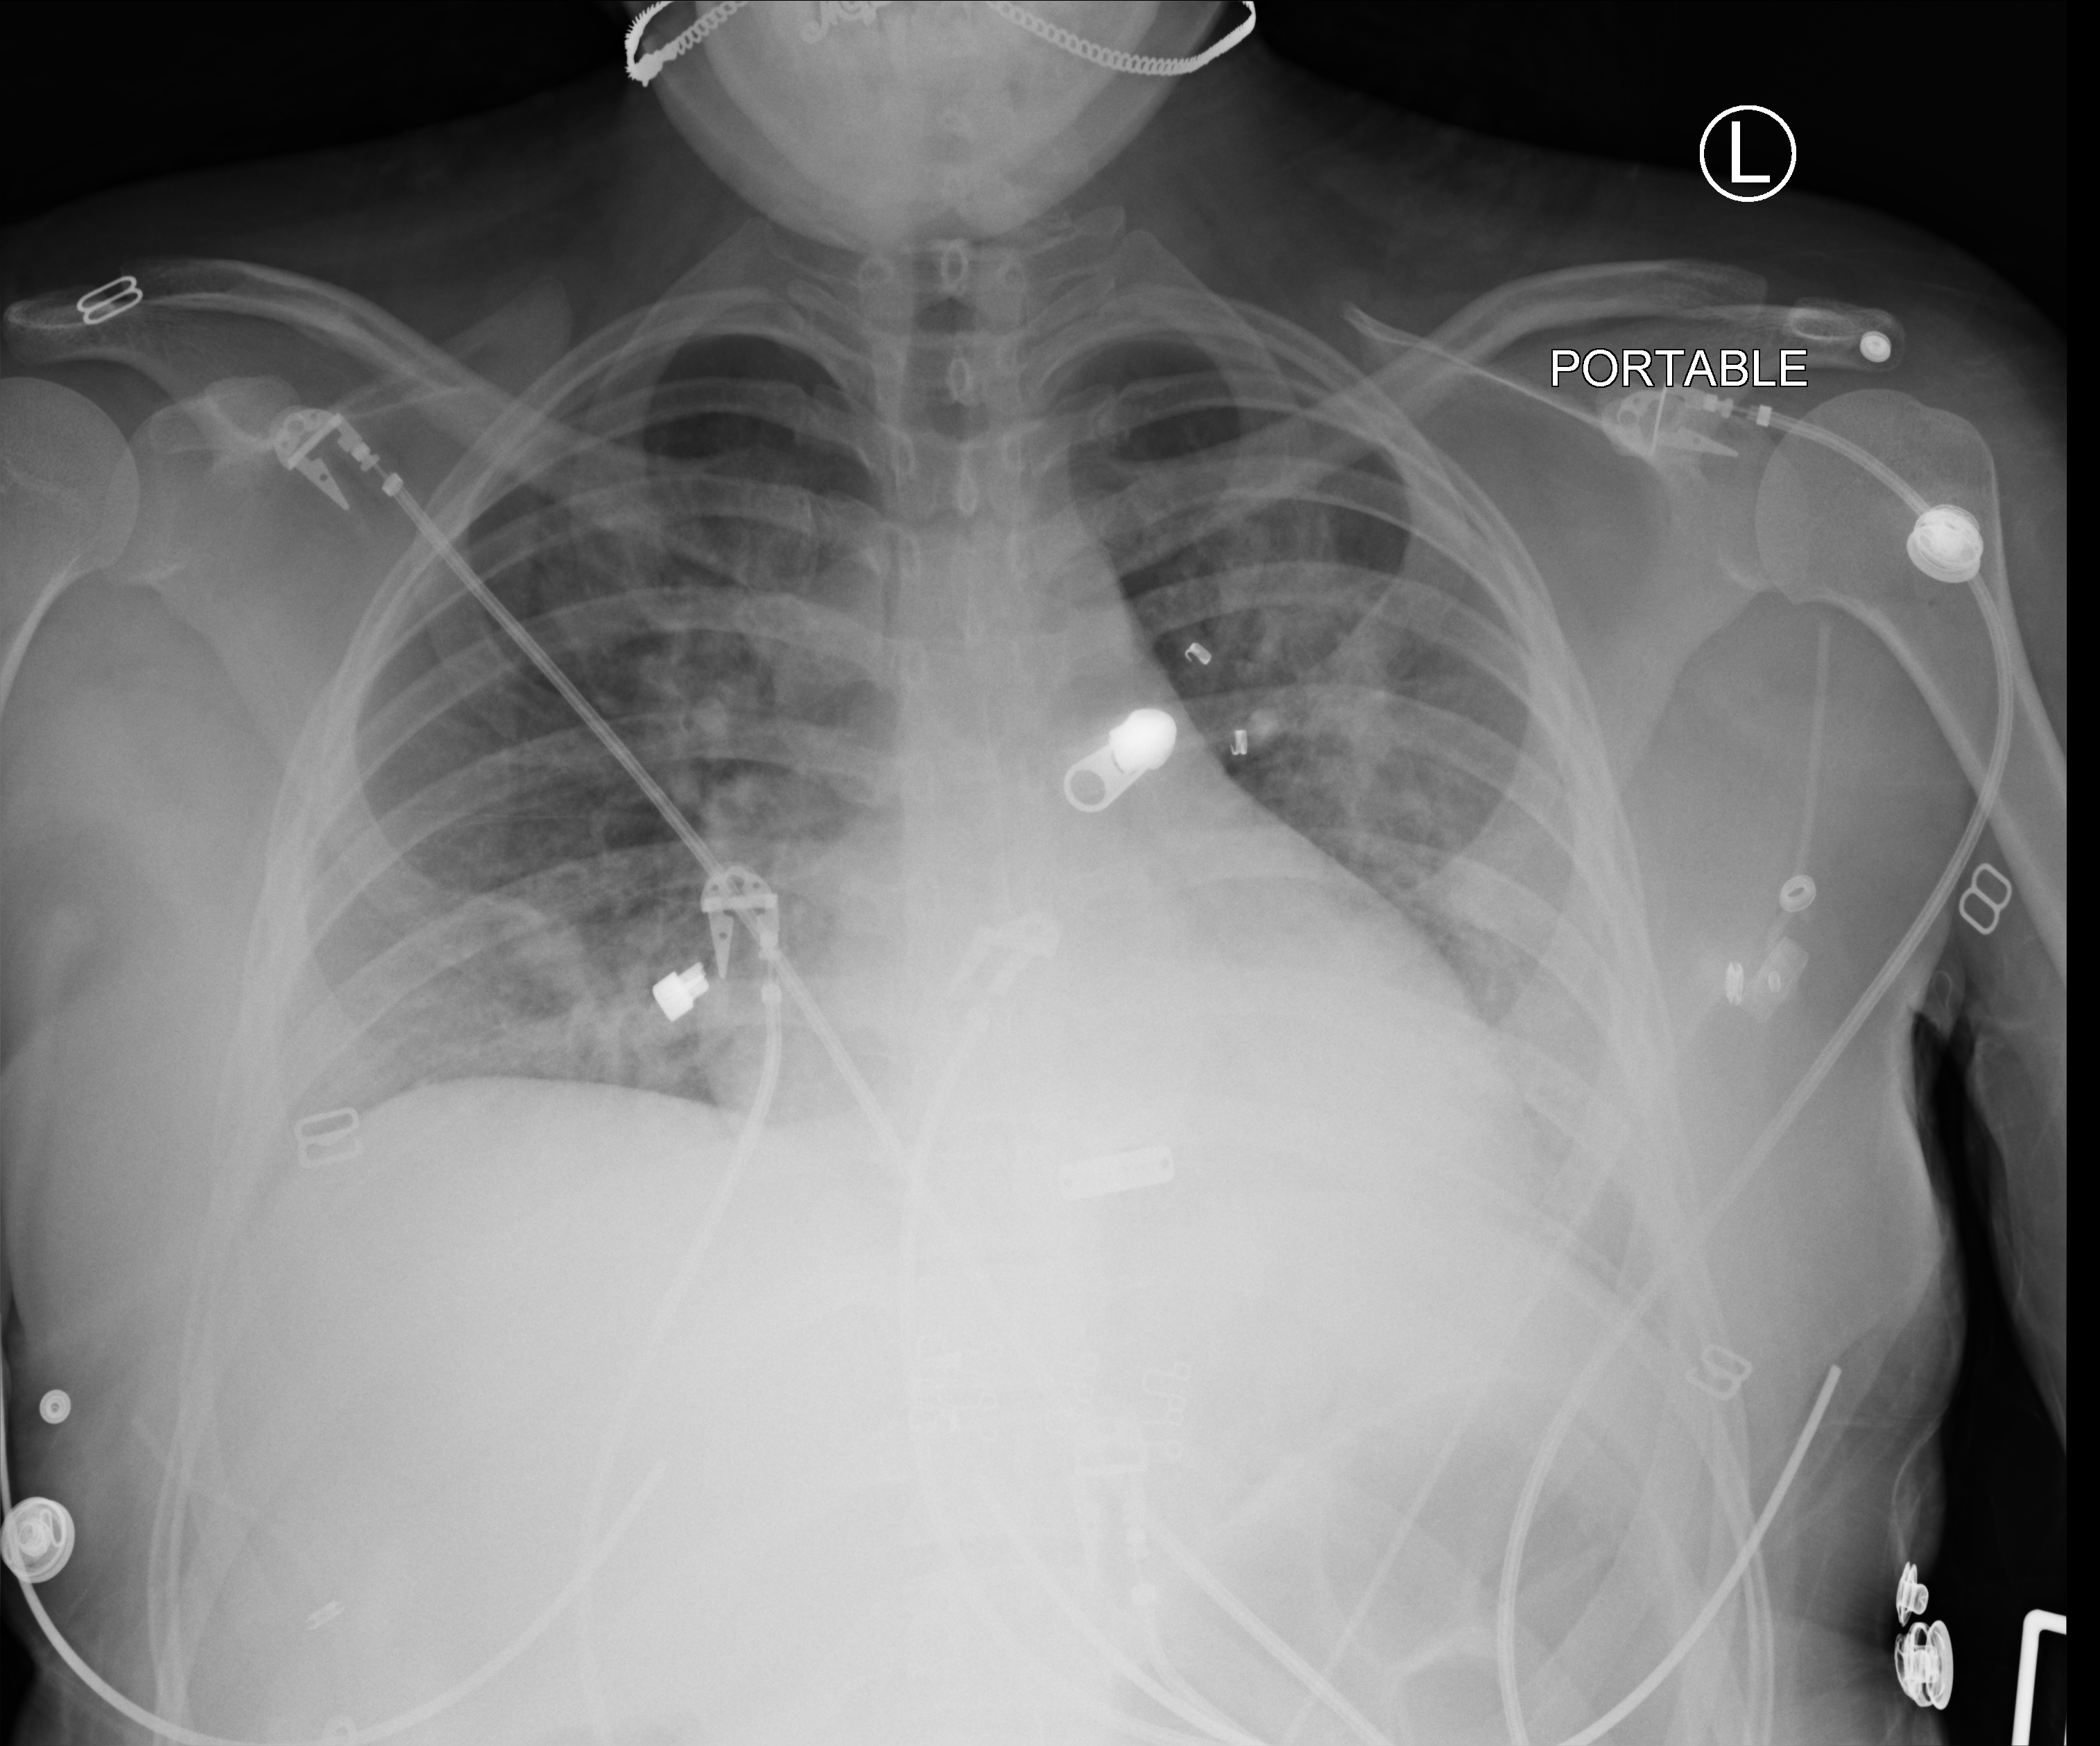
Portable chest radiograph; anteroposterior (AP) projection. Patient hospitalised with COVID-19; female, aged 18–59 years.
Admission-level facts for this patient (not findings on this image; timing relative to this image not recorded): mechanically ventilated during this hospital stay: no; admitted to intensive care during this hospital stay: no.